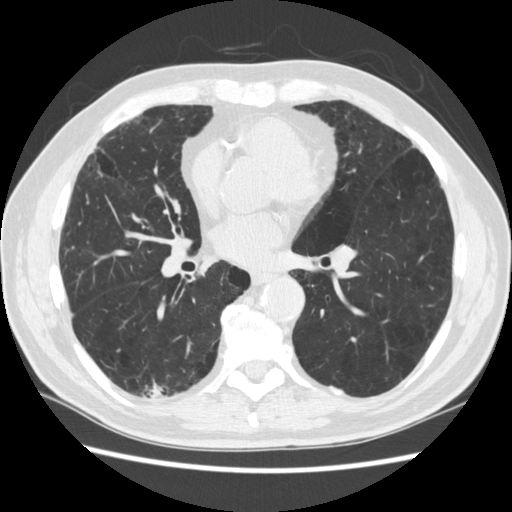
Low-dose screening chest CT, axial slice, third screening round (two years after baseline), lung window (W 1500 / L -600 HU), 1.25 mm slice thickness, 120 kVp, slice 138 of 266 in the series, 512 × 512 image matrix, field of view 360 × 360 mm. Male, age 70 years at enrolment.
- Expert-annotated lung lesion, bounding box (x1, y1, x2, y2) in pixels: (119, 361, 186, 422).
- The screening reader recorded 4 non-calcified nodules or masses ≥4 mm on this exam (right lower lobe, right lower lobe, left lower lobe, left lower lobe); which of them this box marks is not recorded.
- Lung cancer was diagnosed 253 days after this screen: squamous cell carcinoma, NOS, right upper lobe, poorly differentiated (G3), stage IV (AJCC 6th edition).